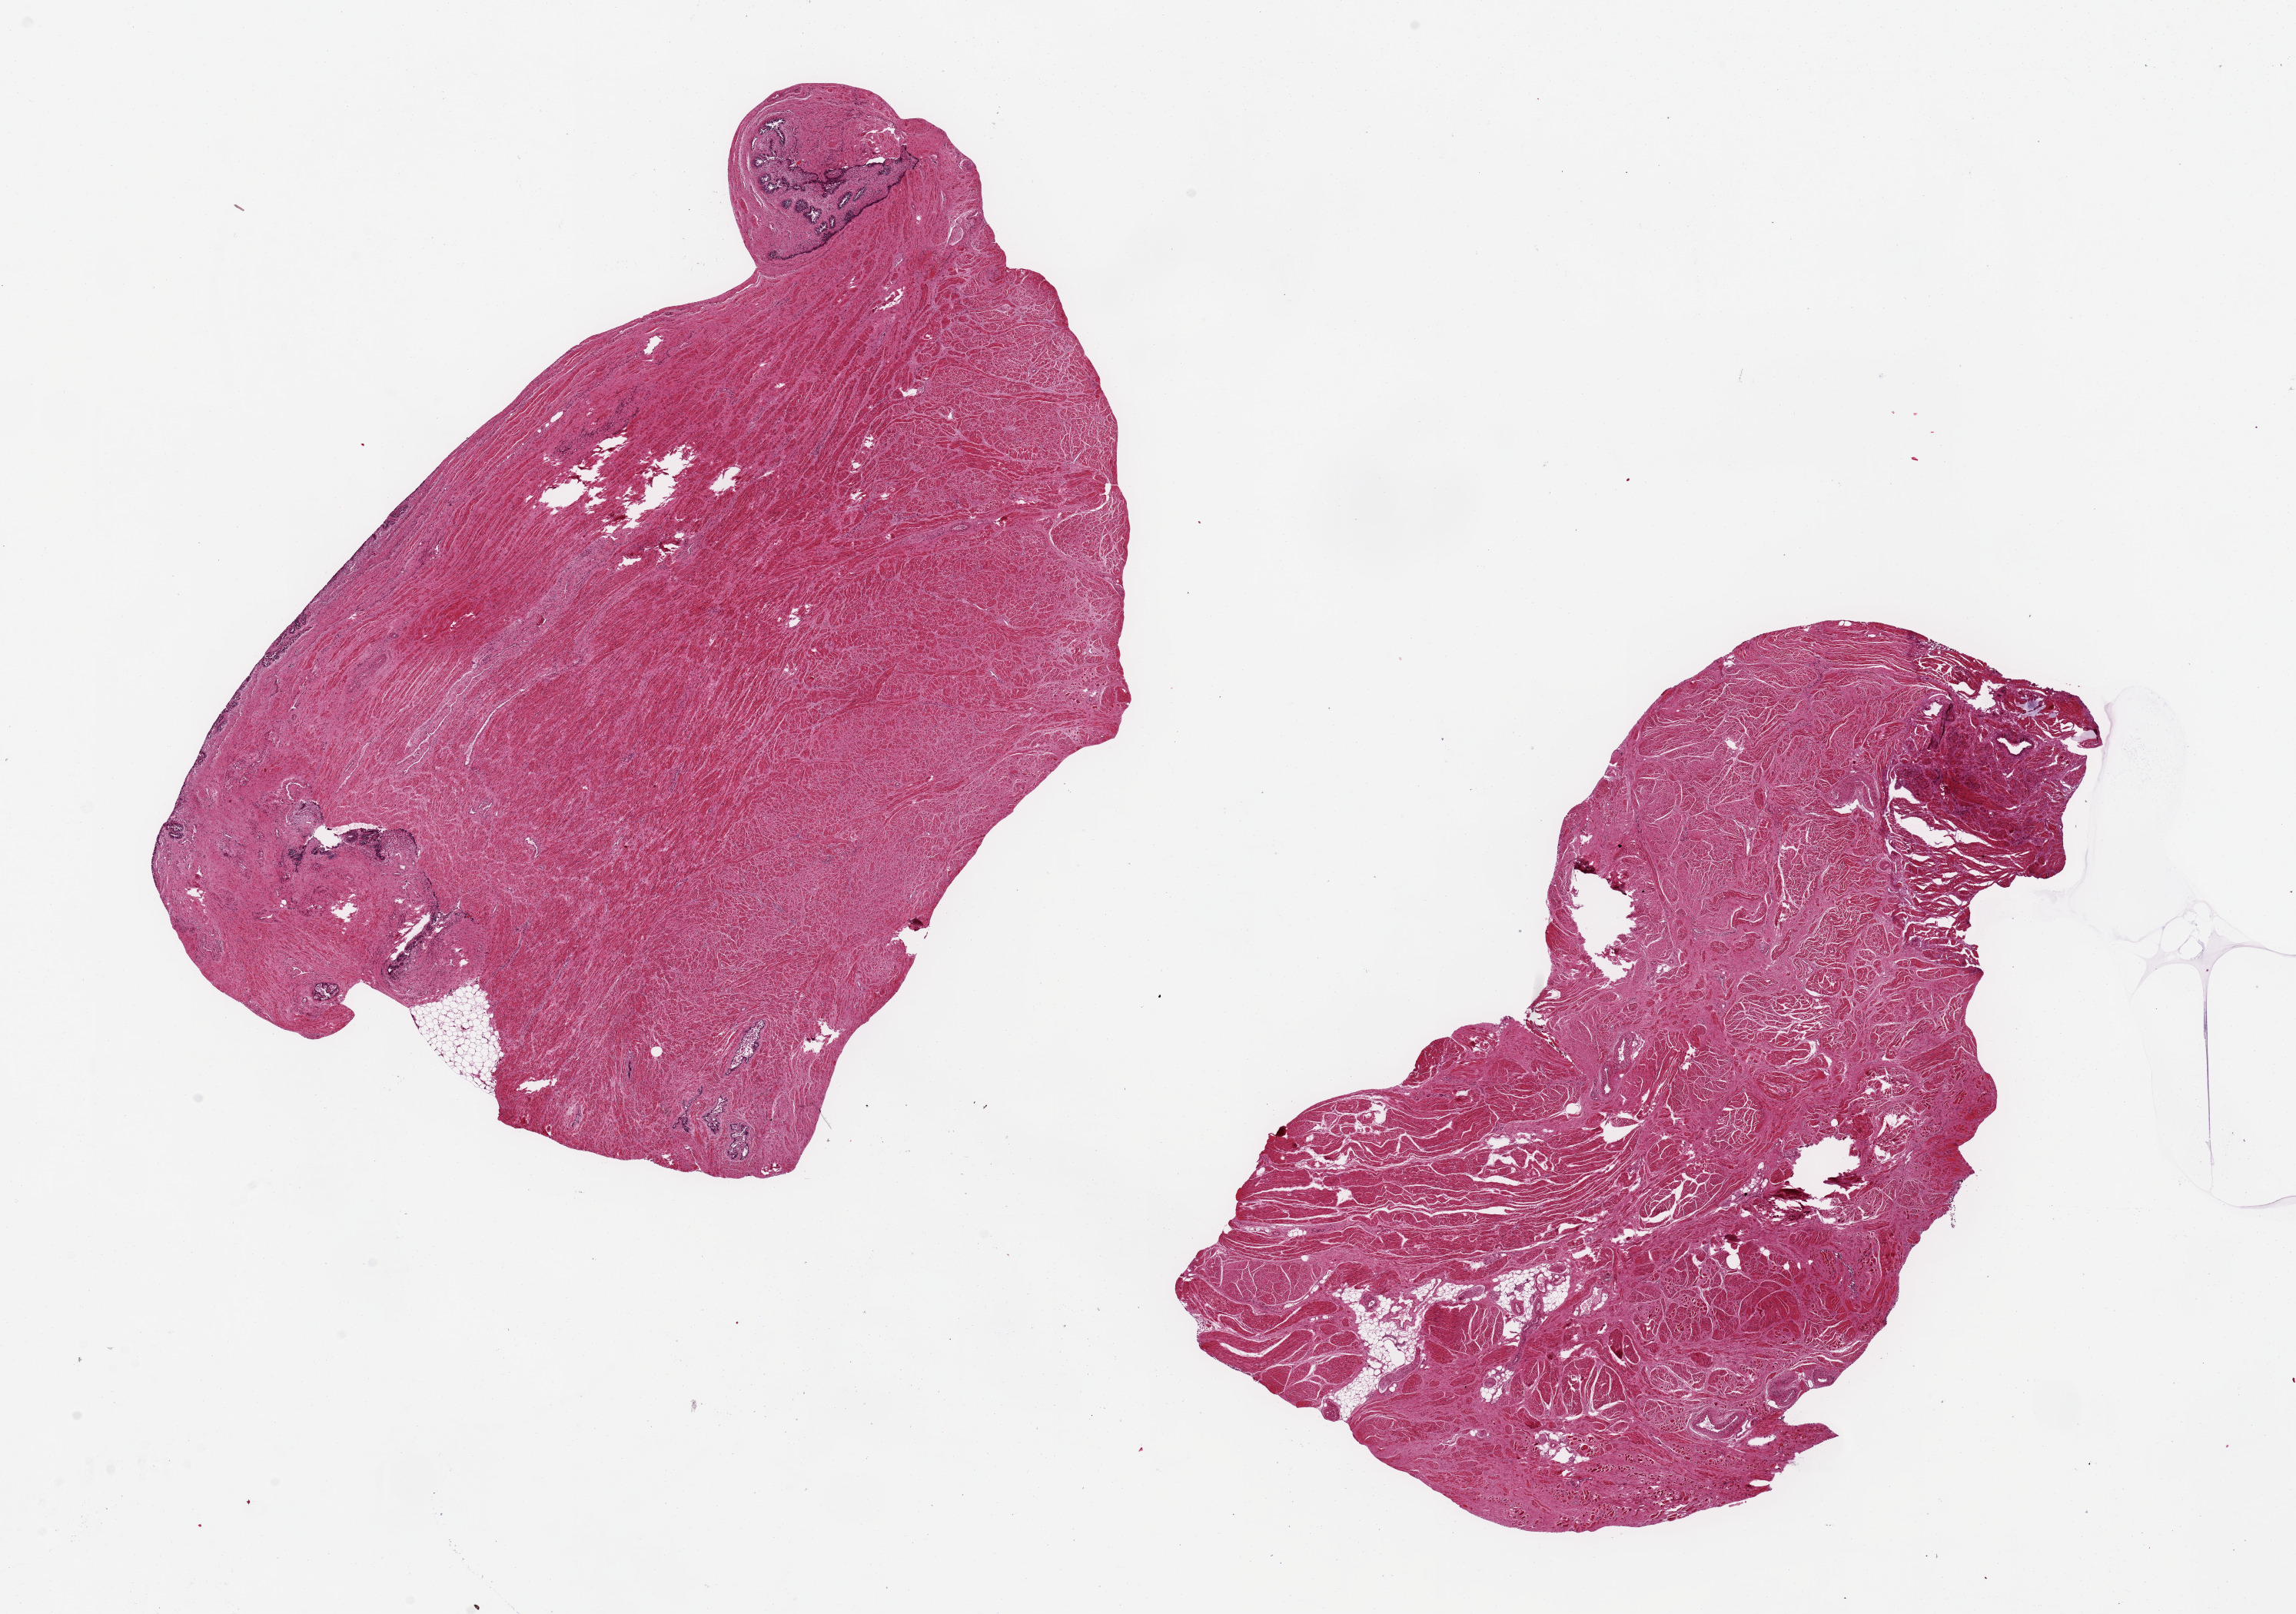
Whole-slide image, hematoxylin and eosin (H&E) stain, shown as a low-resolution overview of the whole scanned area (about 23.6 x 16.6 mm, acquisition: 20x scan), PAXgene-fixed paraffin-embedded (PFPE) section, target tissue: prostate, donor tissue sample. Donor sex: male.
Review note (as recorded): 2 pieces,~11x7 mm; fibromuscular stroma, few glands (probably seminal vesicle) ; other piece resembles bladder wall; tissue tears.